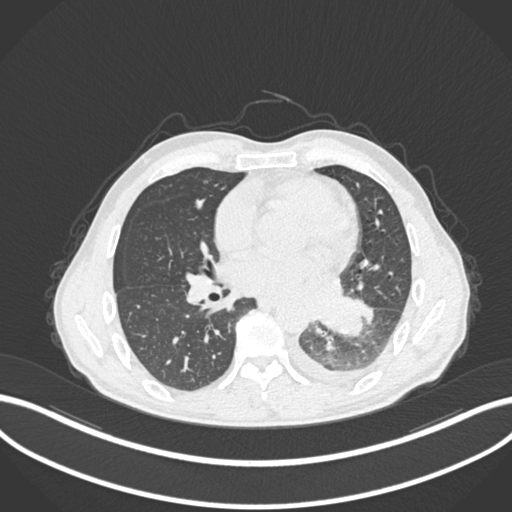
Chest CT, one axial slice; slice 111 of 222 in the series (ordered by position); reconstruction kernel B30f; 120 kVp; lung window (W 1500 / L -600 HU); 1 mm slice thickness; 512 × 512 image matrix. Male patient, age 47 years. Case-level facts recorded for this patient, not image findings: clinical TNM (as recorded): T3 N1 M1c.
Structures marked on this image (bounding box drawn by a radiologist):
- lung tumour (recorded histology: small cell carcinoma): box from (x=316, y=295) to (x=364, y=341) px